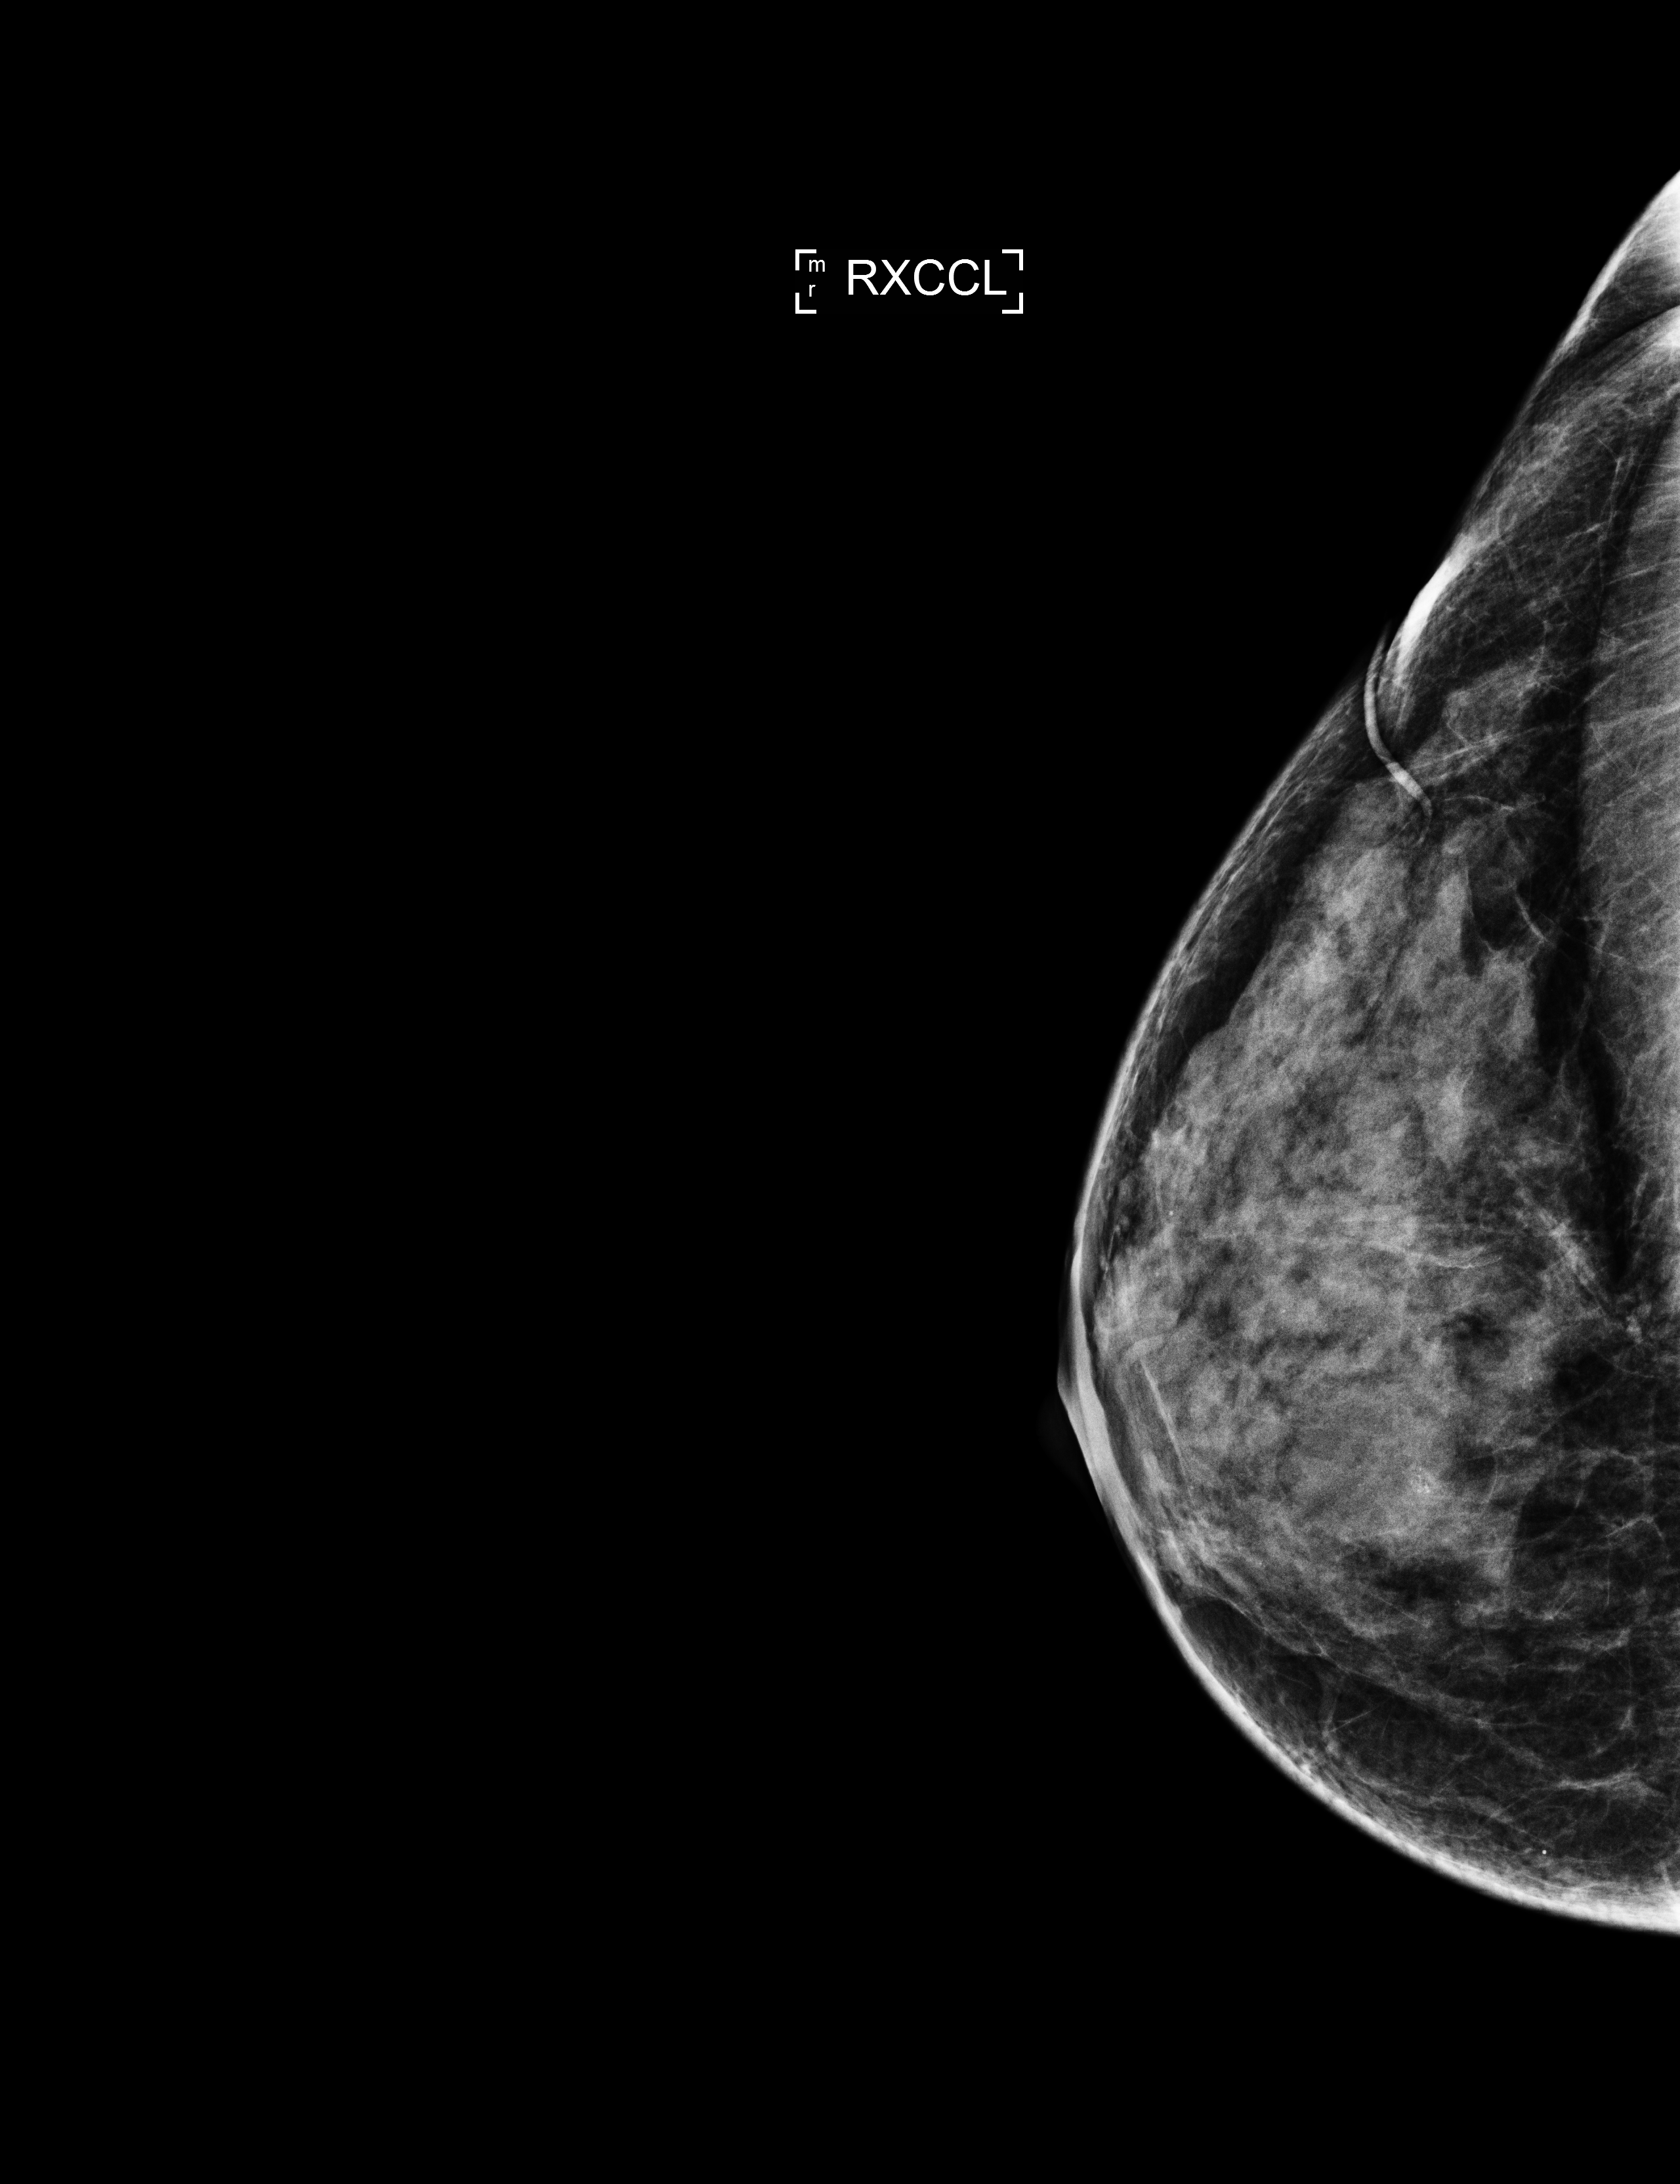
Full-field digital mammogram (FFDM), right breast, laterally exaggerated craniocaudal (XCCL) view, screening examination. Patient aged 50 years (female).
BI-RADS breast density category at the screening exam (both breasts, scale 1–4): 4. Final BI-RADS assessment for this screening round (tomosynthesis exam, both breasts): category 3. Recall: recalled for additional imaging after this screen.